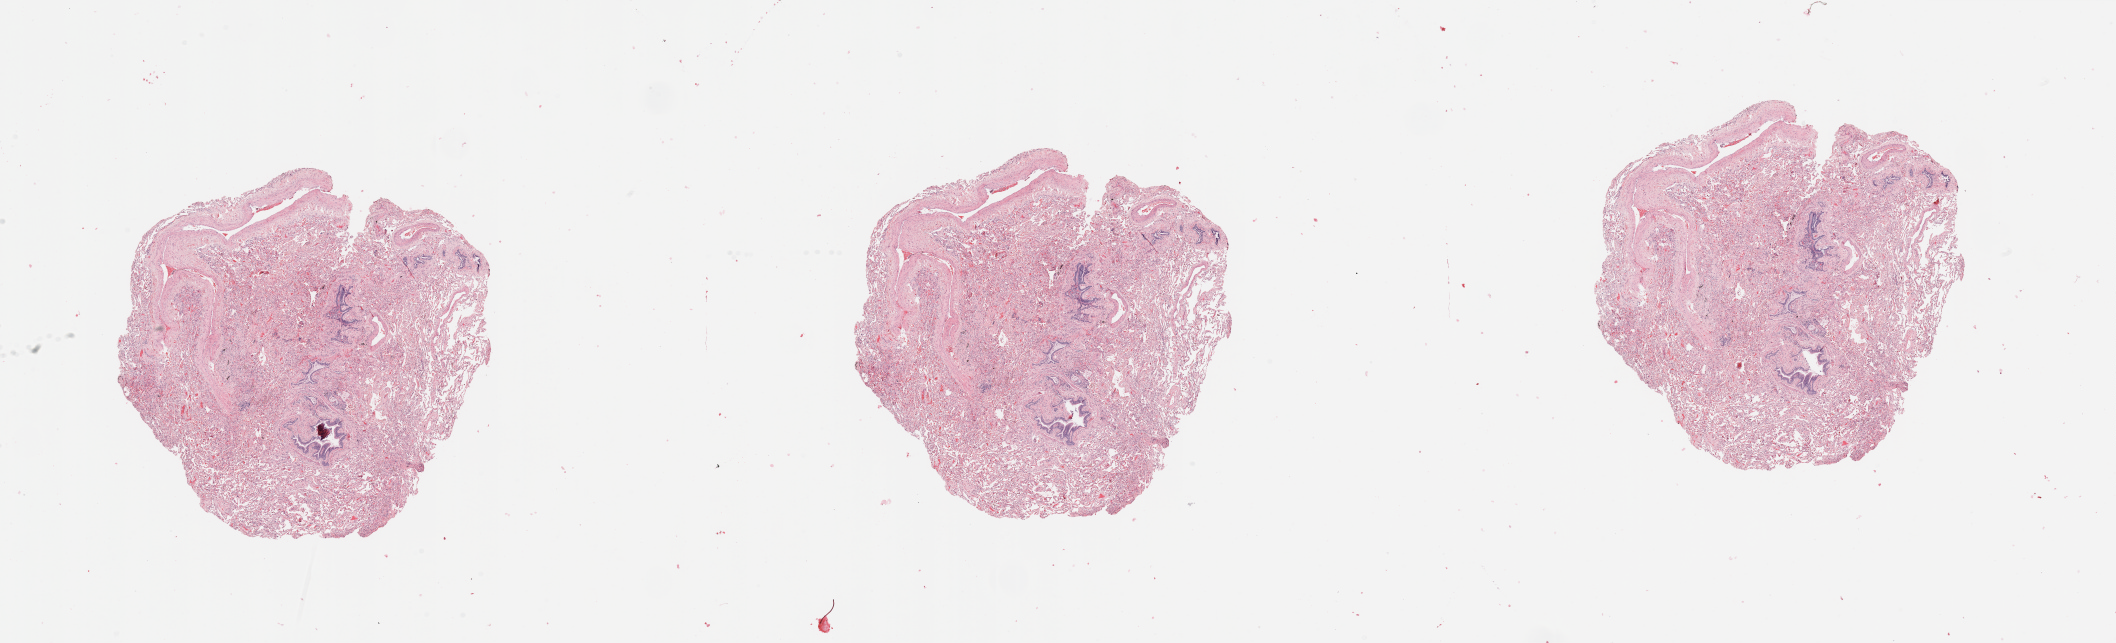
Whole-slide histology image, Hematoxylin and eosin (H&E) stained — a low-resolution overview of the entire scanned area, about 33.5 x 10.2 mm (acquisition: 20x scan), lung, normal (non-tumour) tissue. Patient: female, age 70 years.
This section: normal (non-tumour) tissue from the same patient. Patient diagnosis: Adenocarcinoma, NOS.